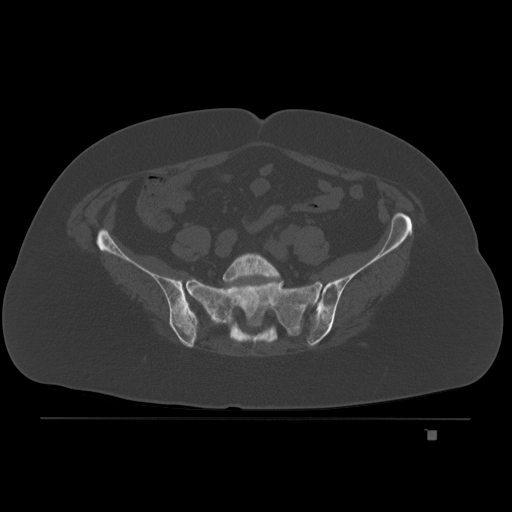
CT including the spine, one axial slice; slice 24 of 221 in the series (ordered by position); bone window (W 1800 / L 400 HU); 3 mm slice thickness; 512 × 512 image matrix, field of view 474 × 474 mm. Patient: female, 63 years. Case-level facts recorded for this patient, not image findings: primary cancer: breast.
Annotated regions visible in this slice (semi-automatic segmentation, software-assisted and operator-edited):
- L5 vertebra: bounding box [x1, y1, x2, y2] px = [223, 252, 281, 284]